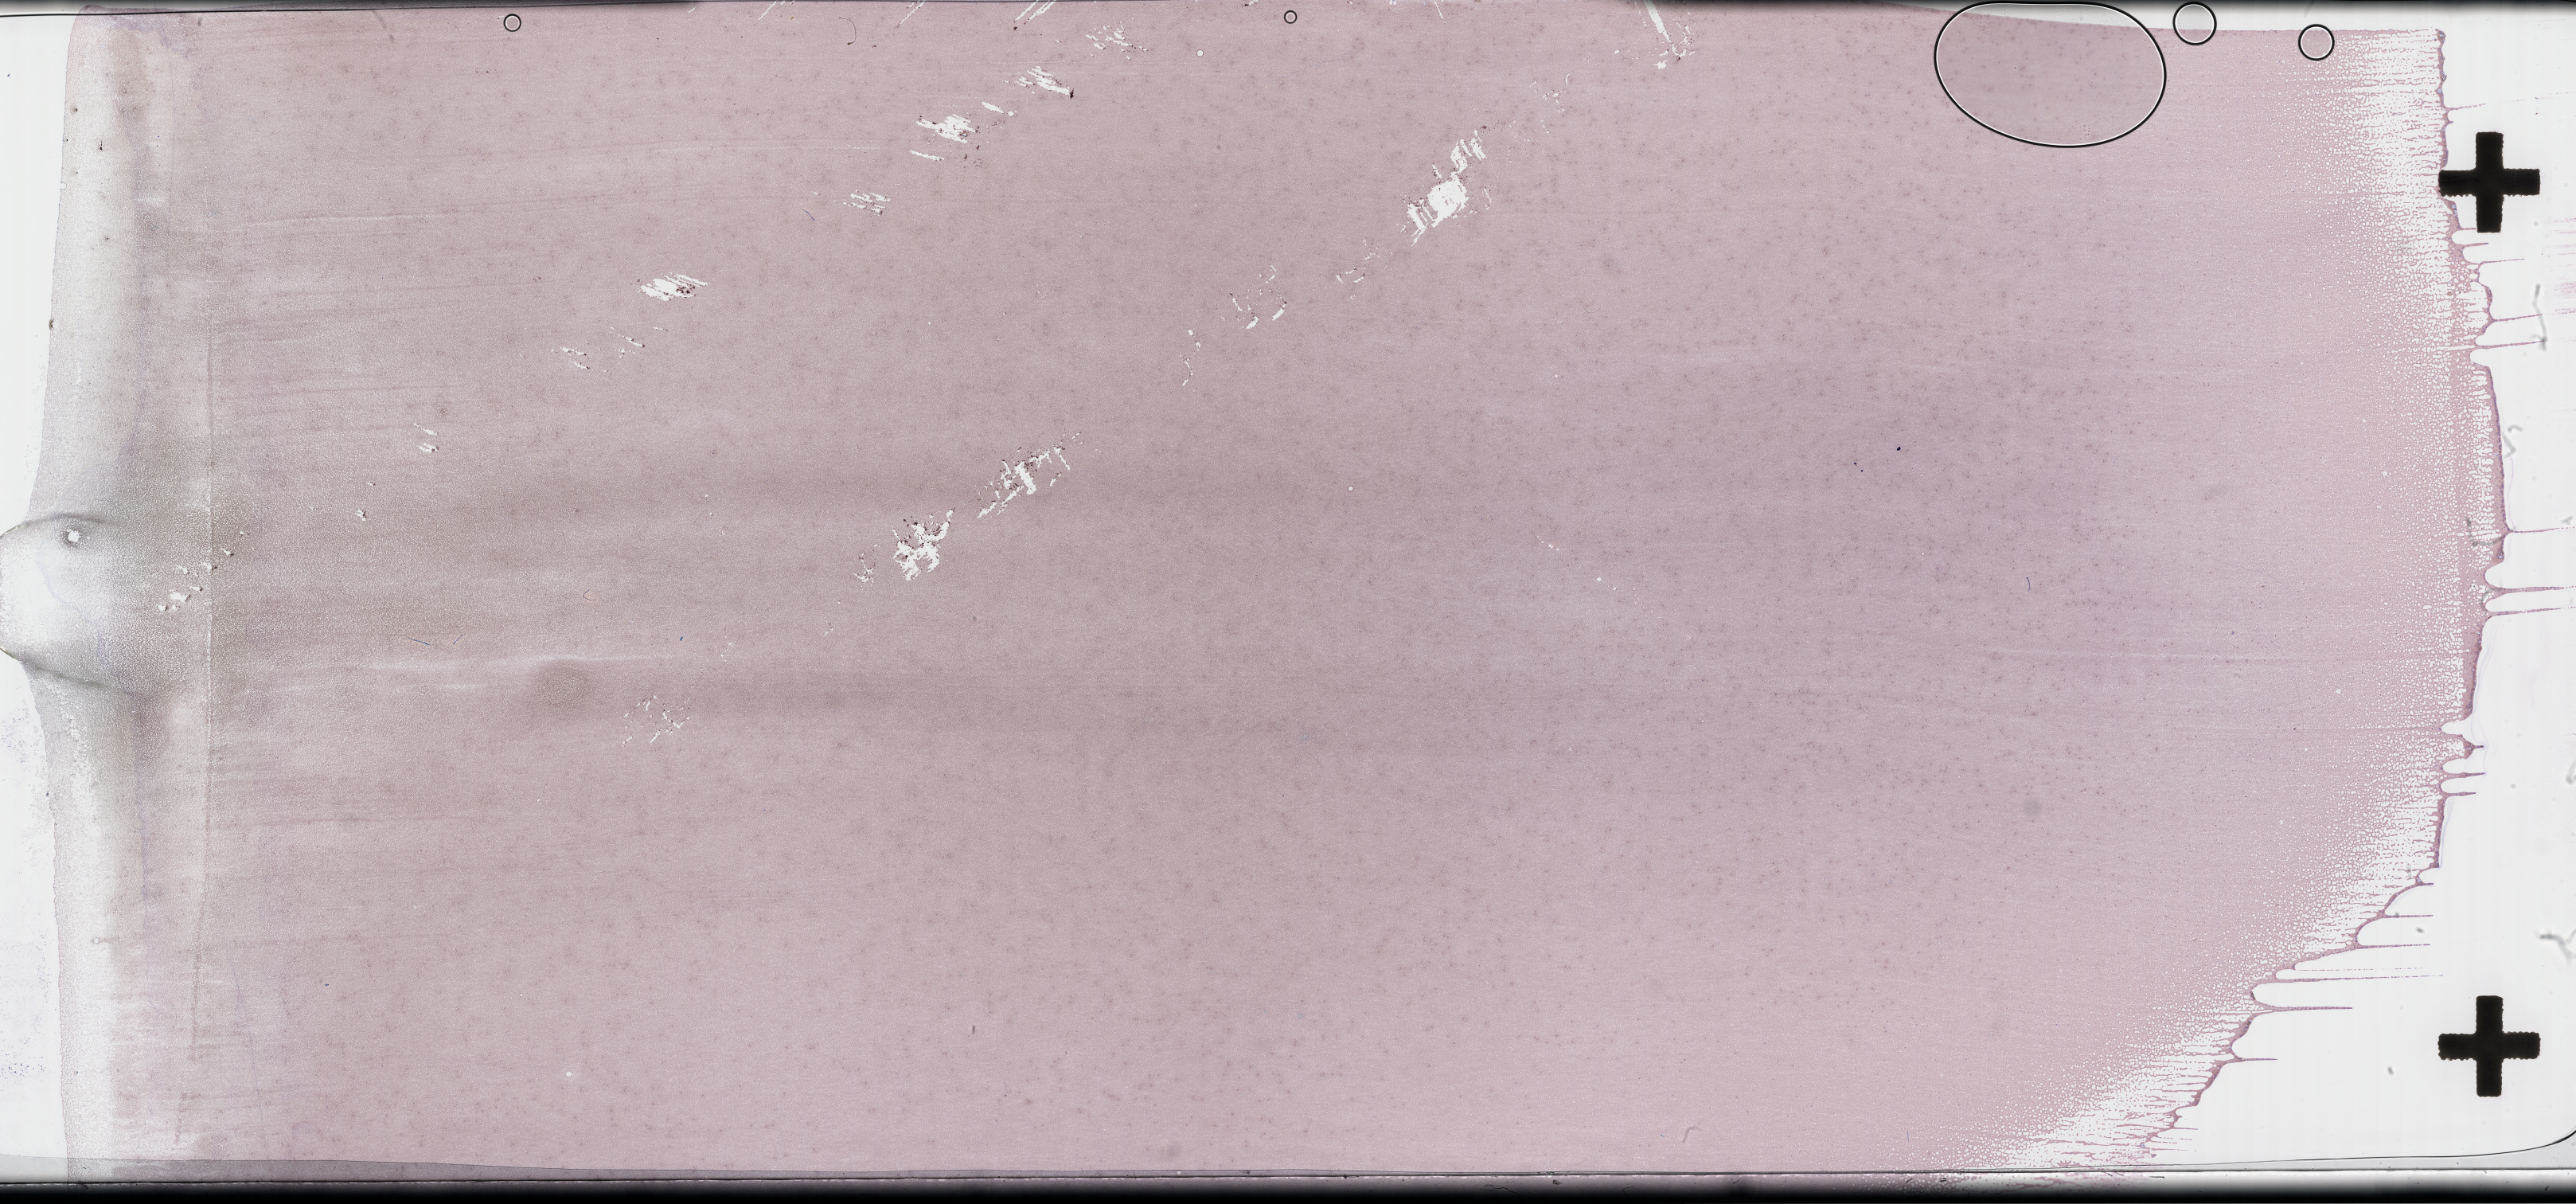
Wright–Giemsa-stained whole blood smear, whole-slide image — a low-resolution overview of the entire scanned area, about 52.3 x 24.4 mm. Collected on treatment. Patient sex: male.
- patient diagnosis: Plasma Cell Myeloma